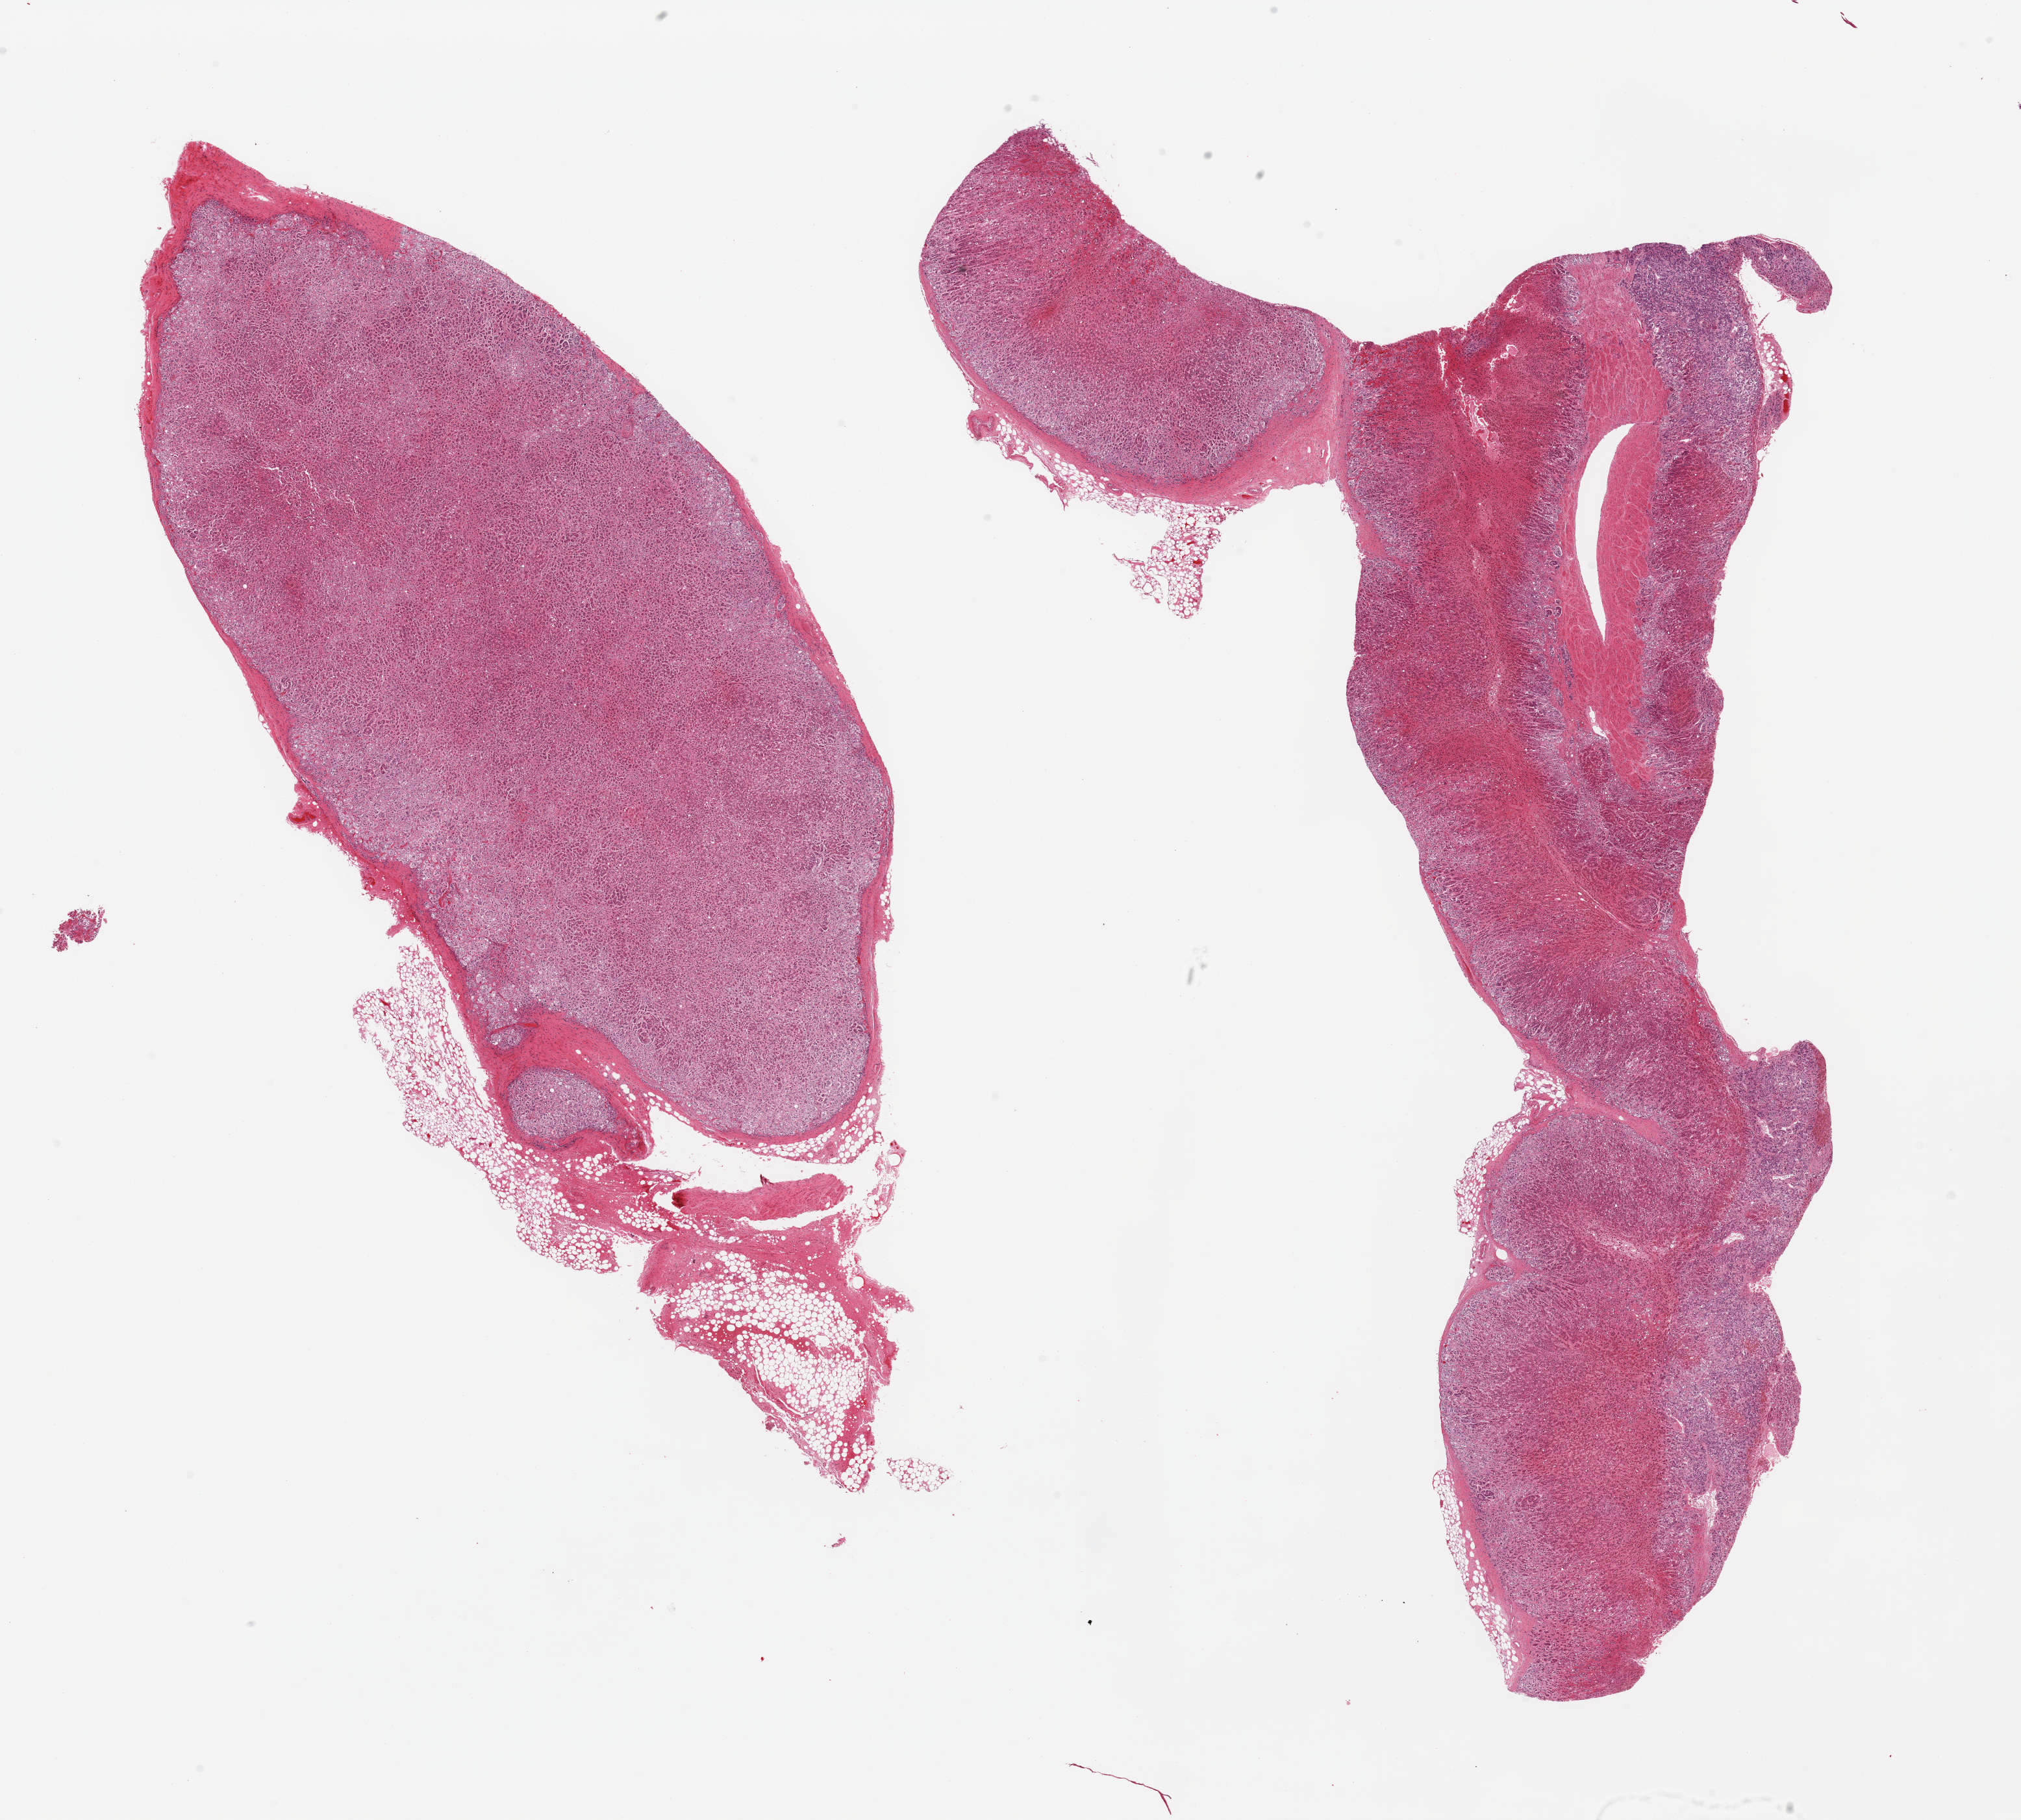
Whole-slide image, hematoxylin and eosin (H&E) stain, whole scanned area (about 24.6 x 22.2 mm) shown as a low-resolution overview, PAXgene-fixed, paraffin-embedded tissue, target tissue: adrenal gland, tissue donor sample. Donor sex: male.
Reviewer comment on this tissue sample: 2 pieces; 10% external fat.